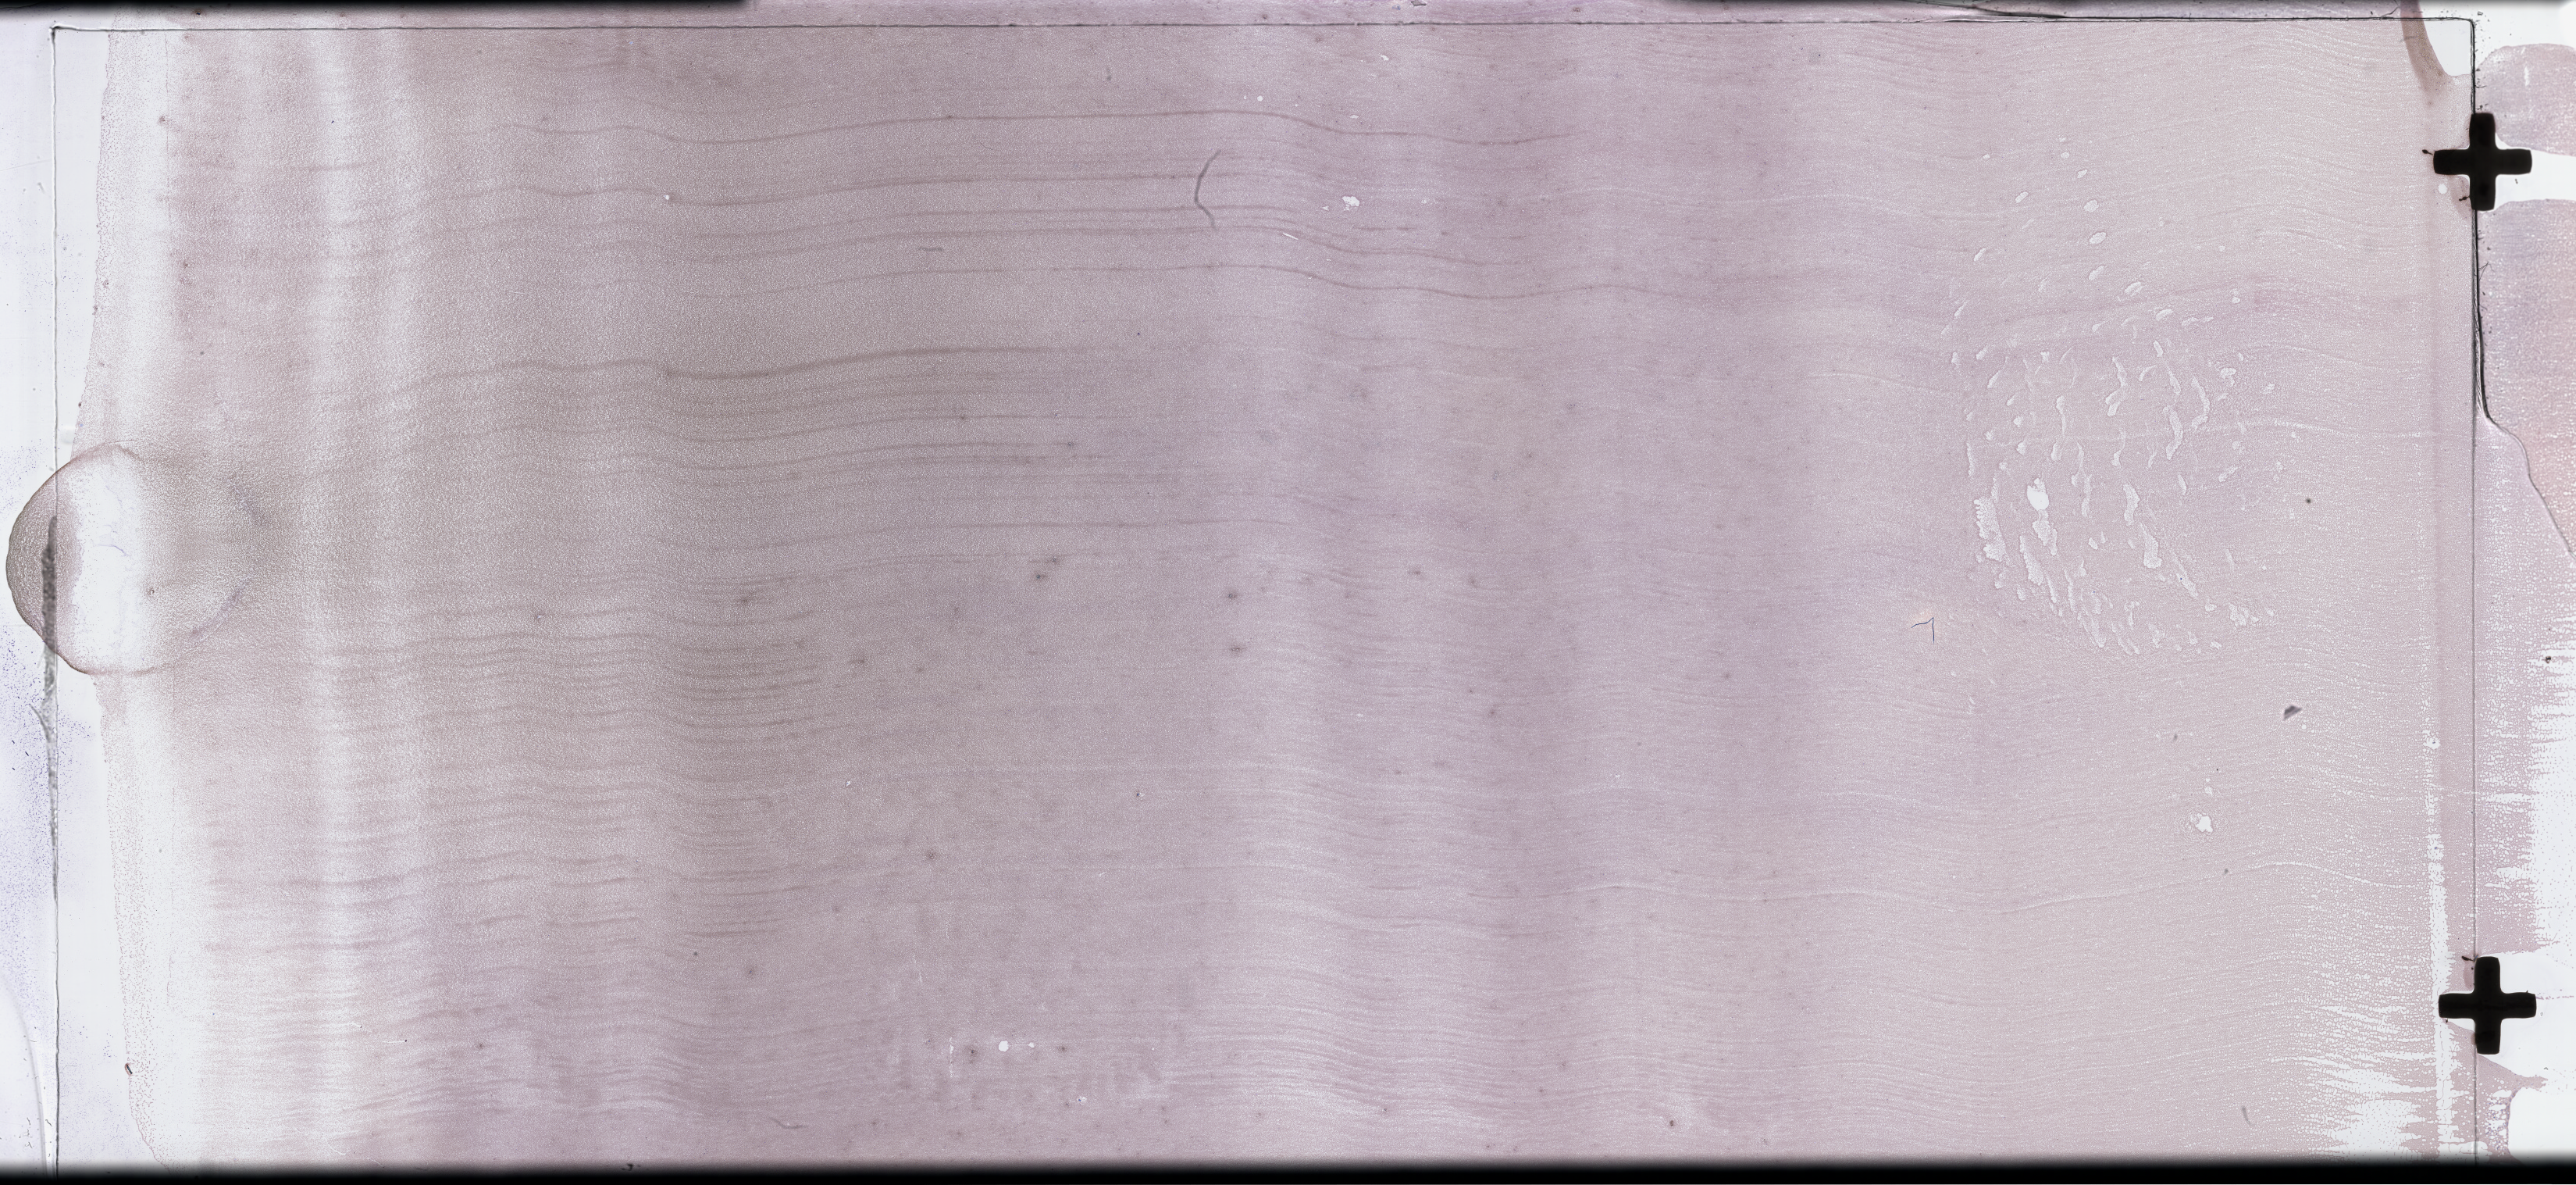
Whole-slide image of a whole blood smear, Wright-Giemsa stain, whole scanned area (about 53.3 x 24.5 mm) shown as a low-resolution overview; smear from an EDTA sample; specimen time point: collected on treatment. Male patient.
From a patient with: Plasma Cell Myeloma.